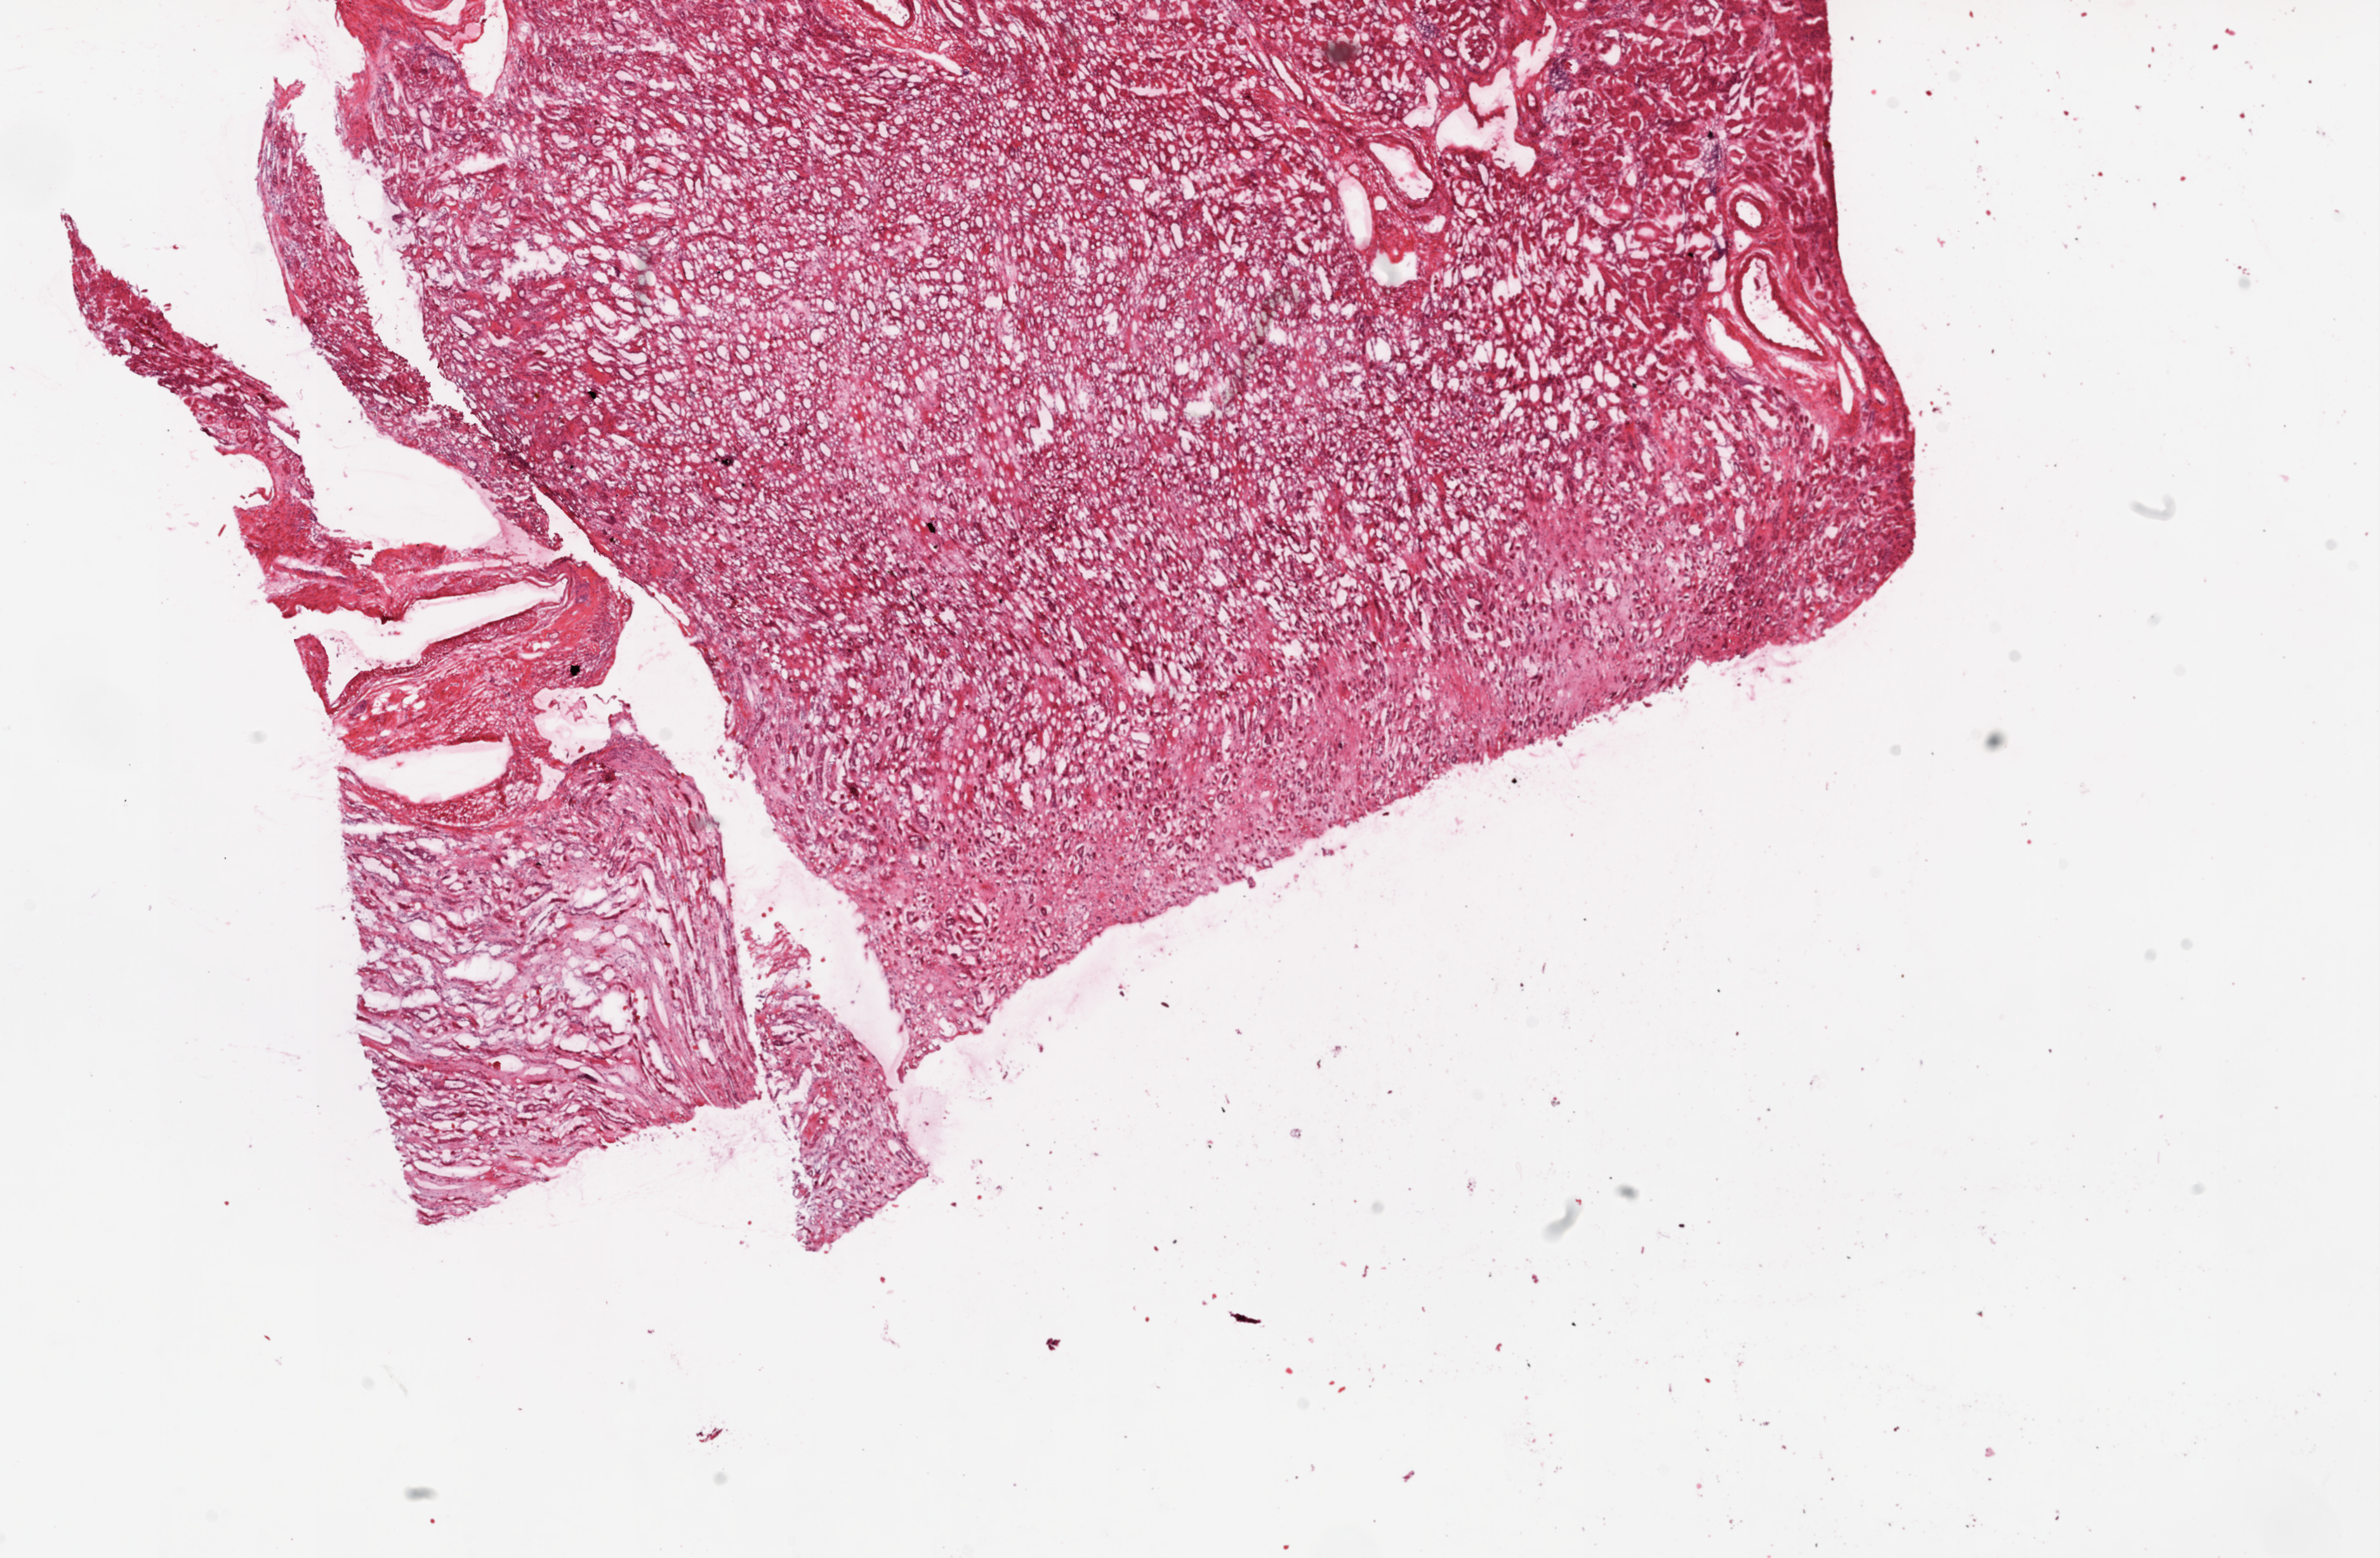
H&E-stained whole-slide image, a low-resolution overview of the entire scanned area, about 15.0 x 9.8 mm (from a 20x scan); frozen section from the top of the tissue portion; kidney, solid tissue normal (non-tumour tissue) sample. Male patient; age at initial diagnosis 60 years.
This section: solid tissue normal sample (biorepository sample class). Patient diagnosis: Clear cell adenocarcinoma, NOS.